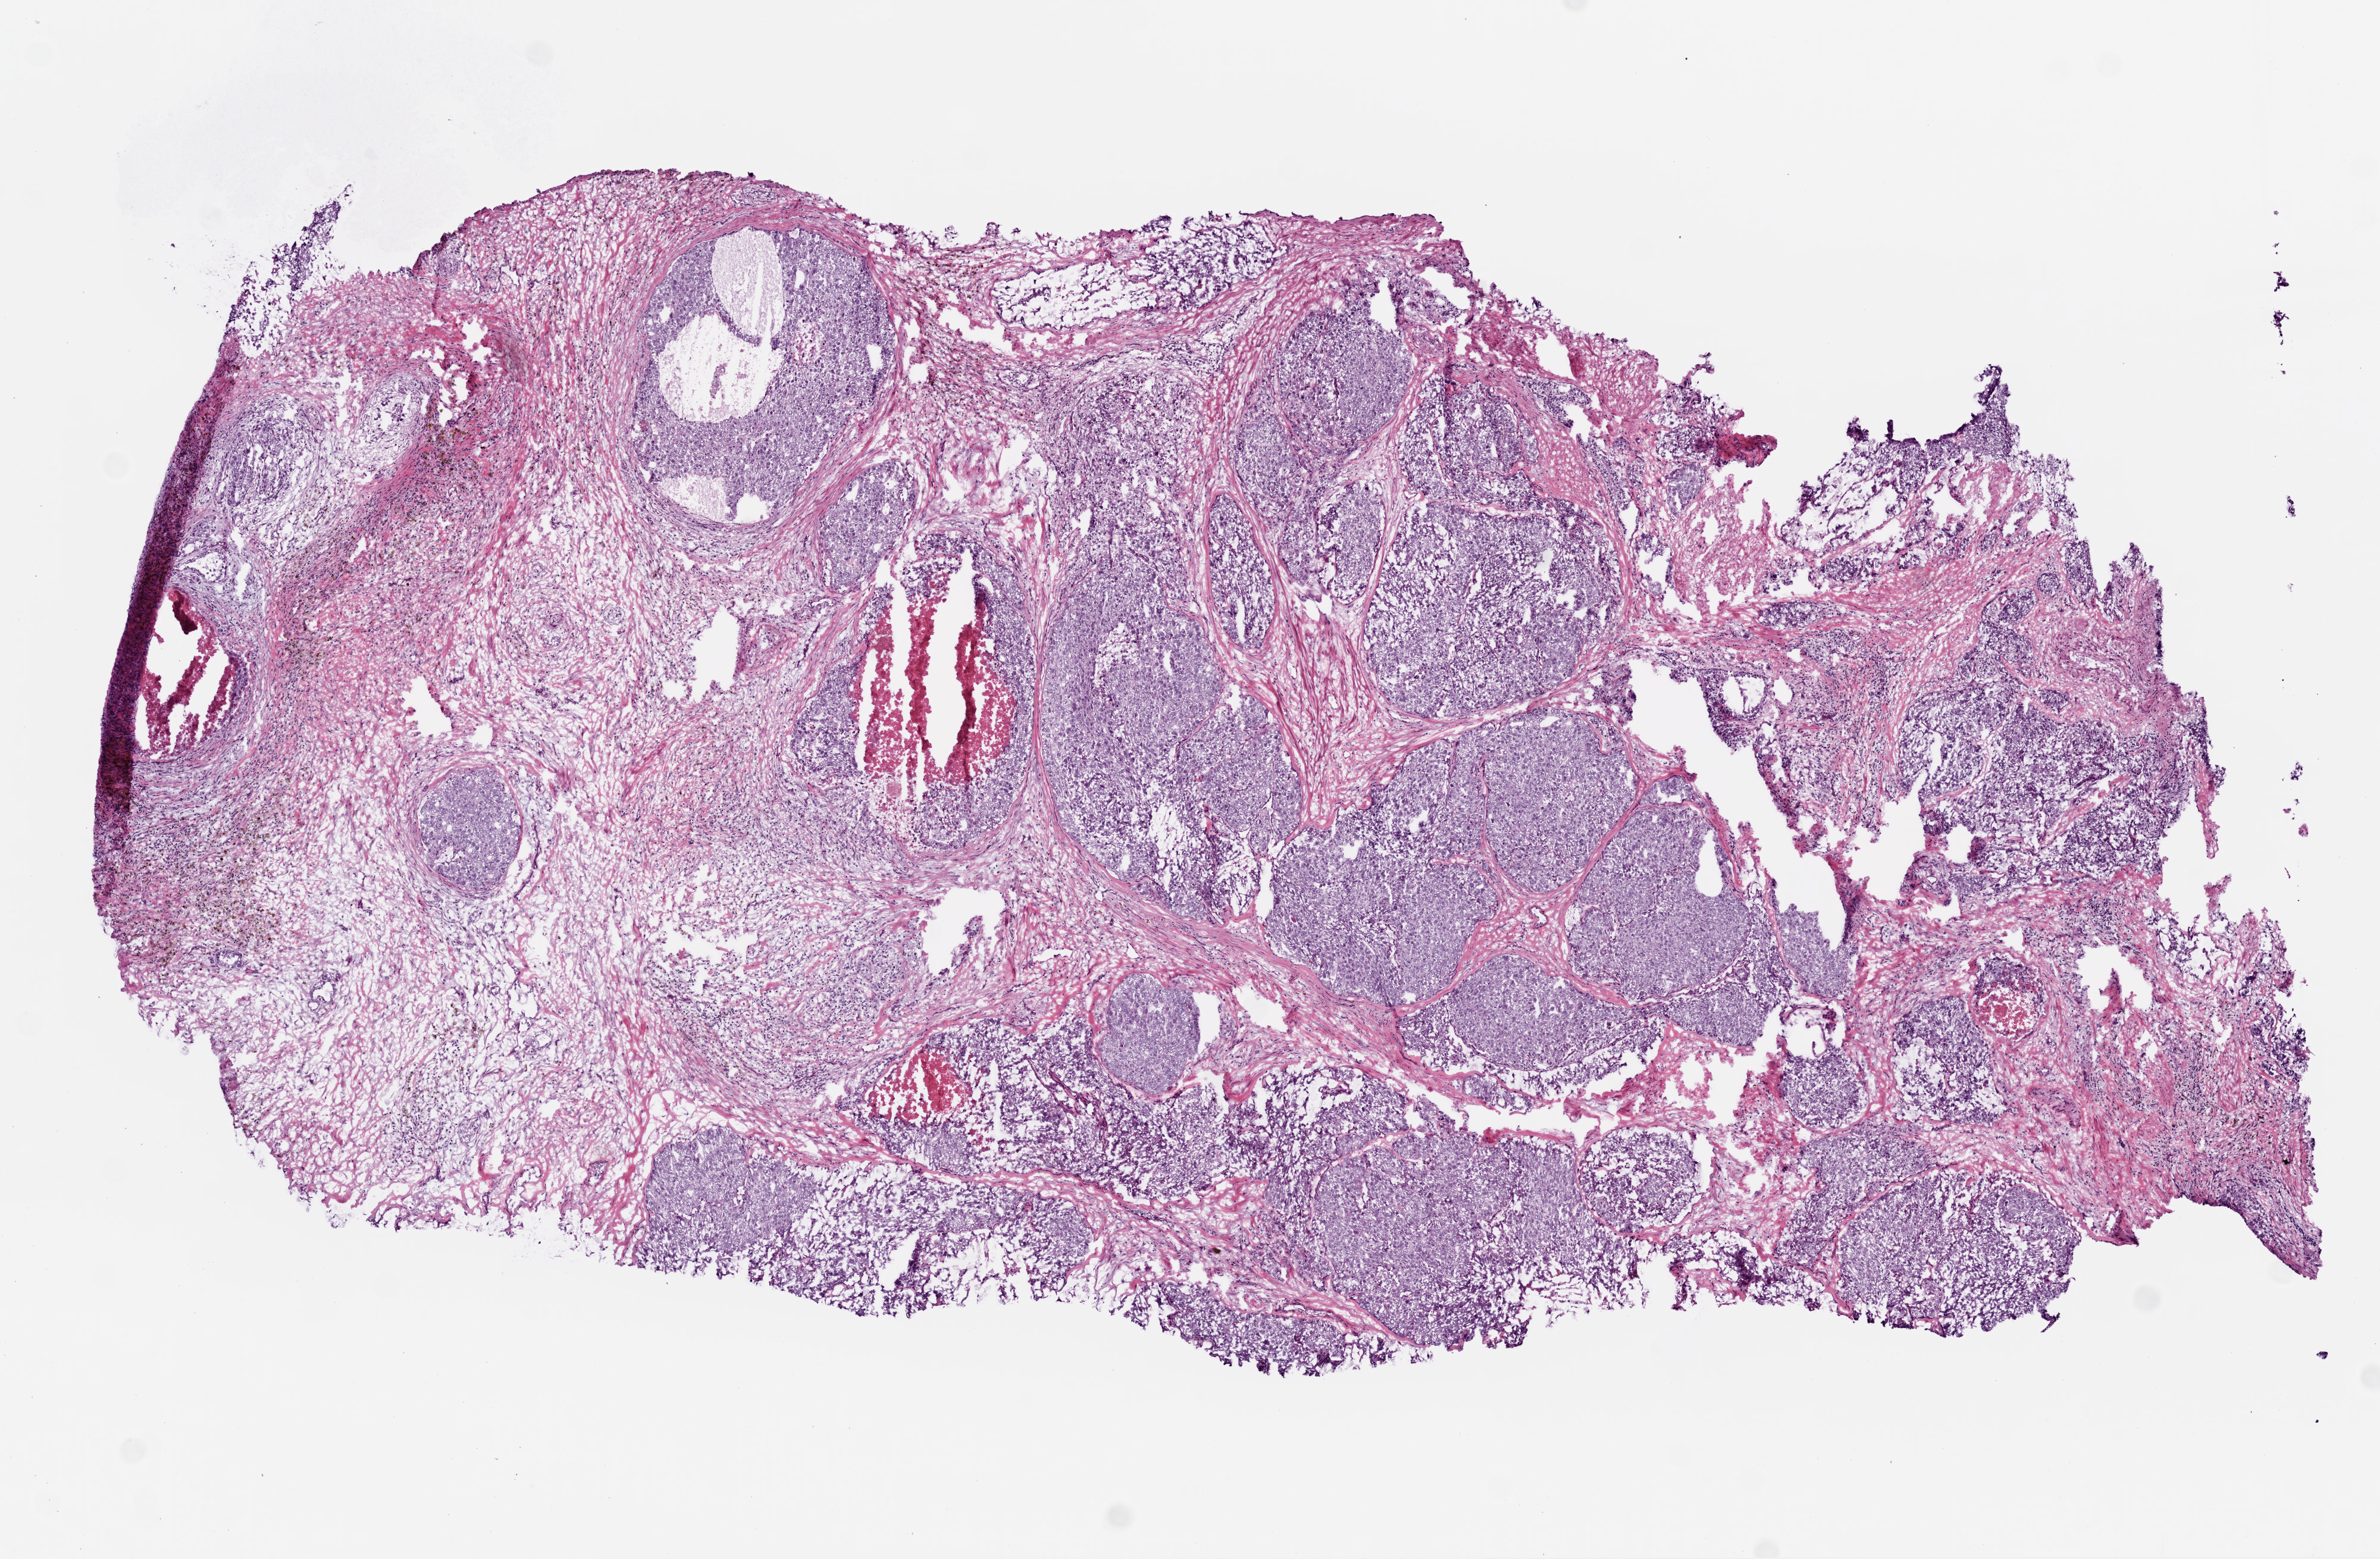
Digitized H&E tissue section (whole slide), whole scanned area (about 8.0 x 5.3 mm, acquisition: 20x scan) shown as a low-resolution overview. Frozen section from the top of the tissue portion. Sample: primary tumour, prostate. Male patient; age at initial diagnosis 61 years.
Pathologic diagnosis: Acinar cell carcinoma (prostate gland).